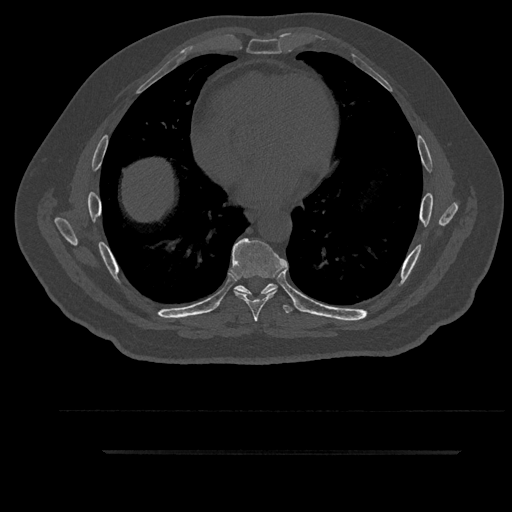
CT including the spine, one axial slice; slice 508 of 797 in the series (ordered by position); 120 kVp; bone window (W 1800 / L 400 HU); 0.5 mm slice thickness; 512 × 512 image matrix, field of view 432 × 432 mm. Patient: male, 63 years. Case-level facts recorded for this patient, not image findings: primary cancer: renal; vertebrae with lytic lesions (as recorded): T8.
Structures marked on this image (semi-automatically segmented with operator editing):
- T6 vertebra: bounding box [x1, y1, x2, y2] px = [241, 291, 270, 296]
- T7 vertebra: [230, 238, 288, 322]
- T8 vertebra: [216, 284, 302, 313]